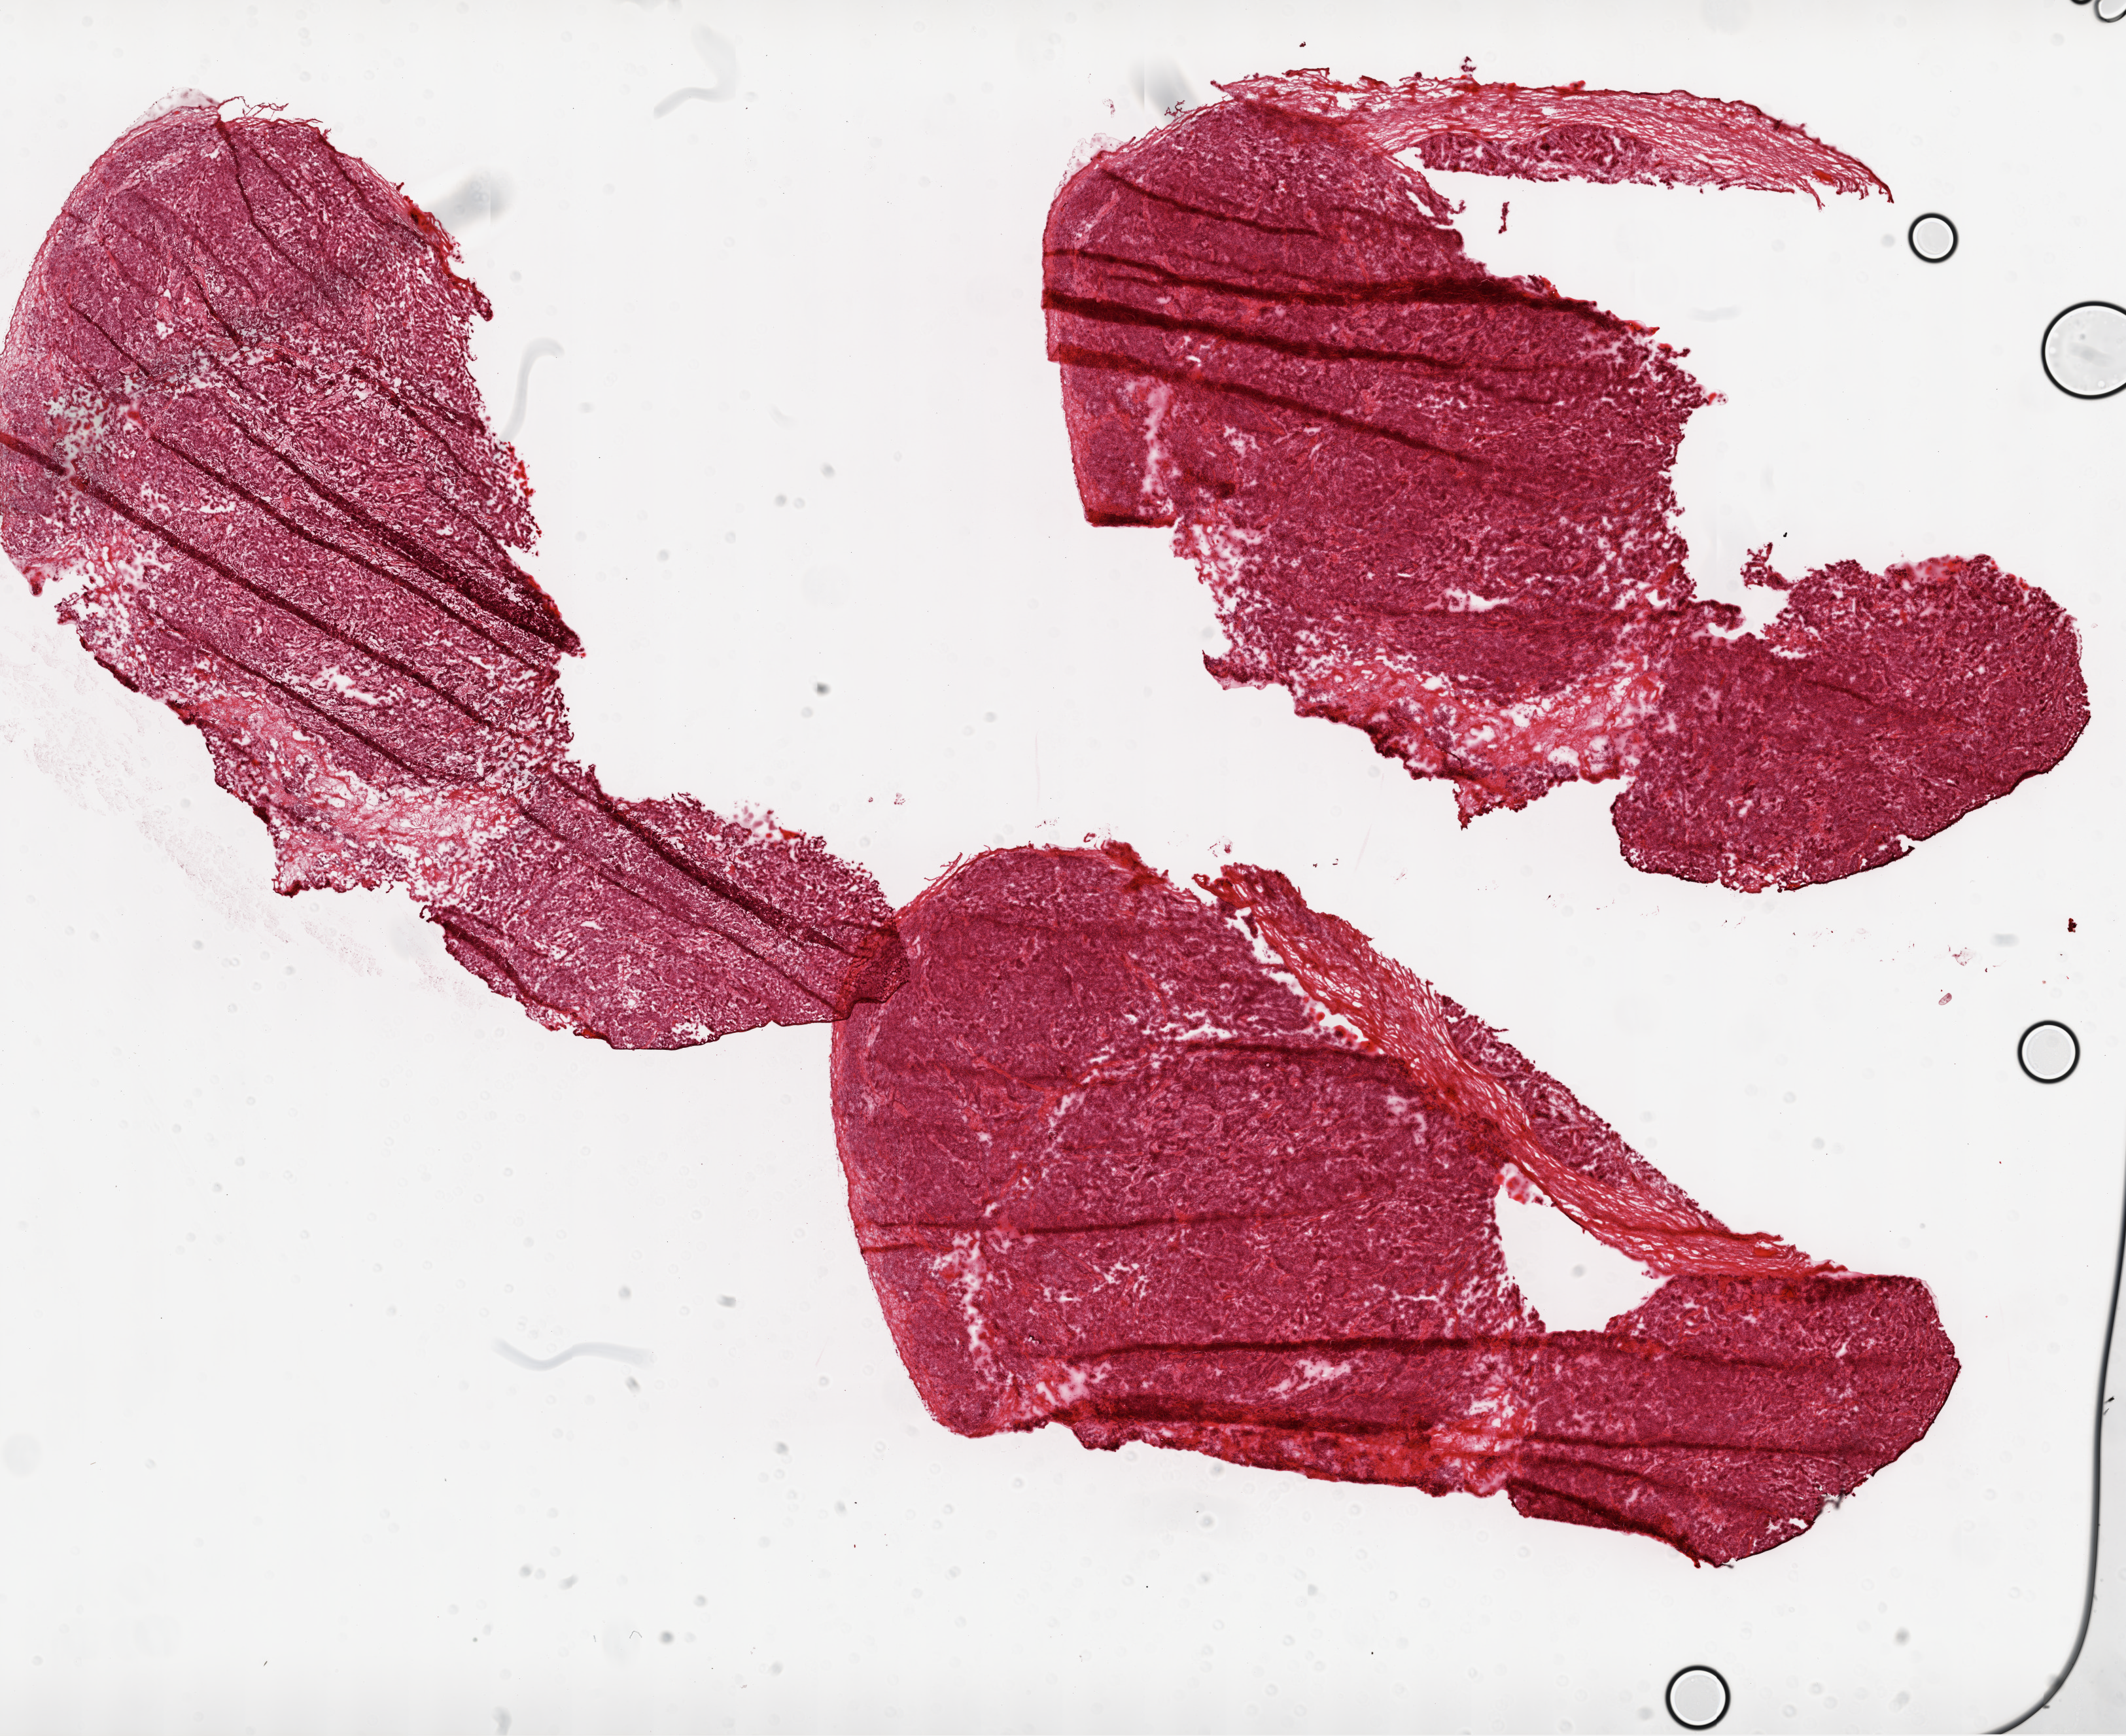
Hematoxylin and eosin (H&E) stained whole-slide image — a low-resolution overview of the entire scanned area, about 26.1 x 21.3 mm (acquisition: 20x scan). Frozen section. Sample: primary tumour, ovary. Patient: female, age at initial diagnosis 53 years. Histologic grade: G3 (poorly differentiated). Slide review estimates, as recorded: tumour cells 95%, tumour nuclei 99%, normal cells 0%, stromal cells 5%, necrosis 0%.
• FIGO stage: IIIB
• histologic diagnosis: Serous cystadenocarcinoma, NOS